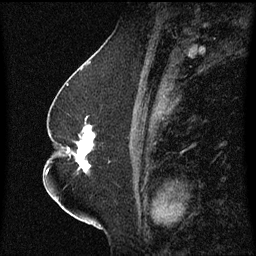
Breast MRI (dynamic contrast-enhanced), one sagittal slice; position 31 of 60 along the scan axis; dynamic contrast-enhanced series, image 2 of 3 at this slice position (ordered by acquisition); 1.5 T; TE 4.2 ms, TR 8.4 ms; 2.3 mm slice thickness; 256 × 256 image matrix, field of view 200 × 200 mm. Female patient, age 52 years. Case-level facts recorded for this patient, not image findings: setting: breast cancer imaged before/during neoadjuvant chemotherapy; receptor status: HR-positive, HER2-negative.
Structures marked on this image (semi-automatic segmentation, software-assisted and operator-edited):
- analysis volume of interest (the breast-tissue region the enhancement analysis was run in; not a lesion): box from (x=65, y=122) to (x=111, y=175) px
- tumour enhancement mask (voxels above the 70 % enhancement threshold inside the analysis volume of interest): (x=69, y=126)–(x=96, y=173)